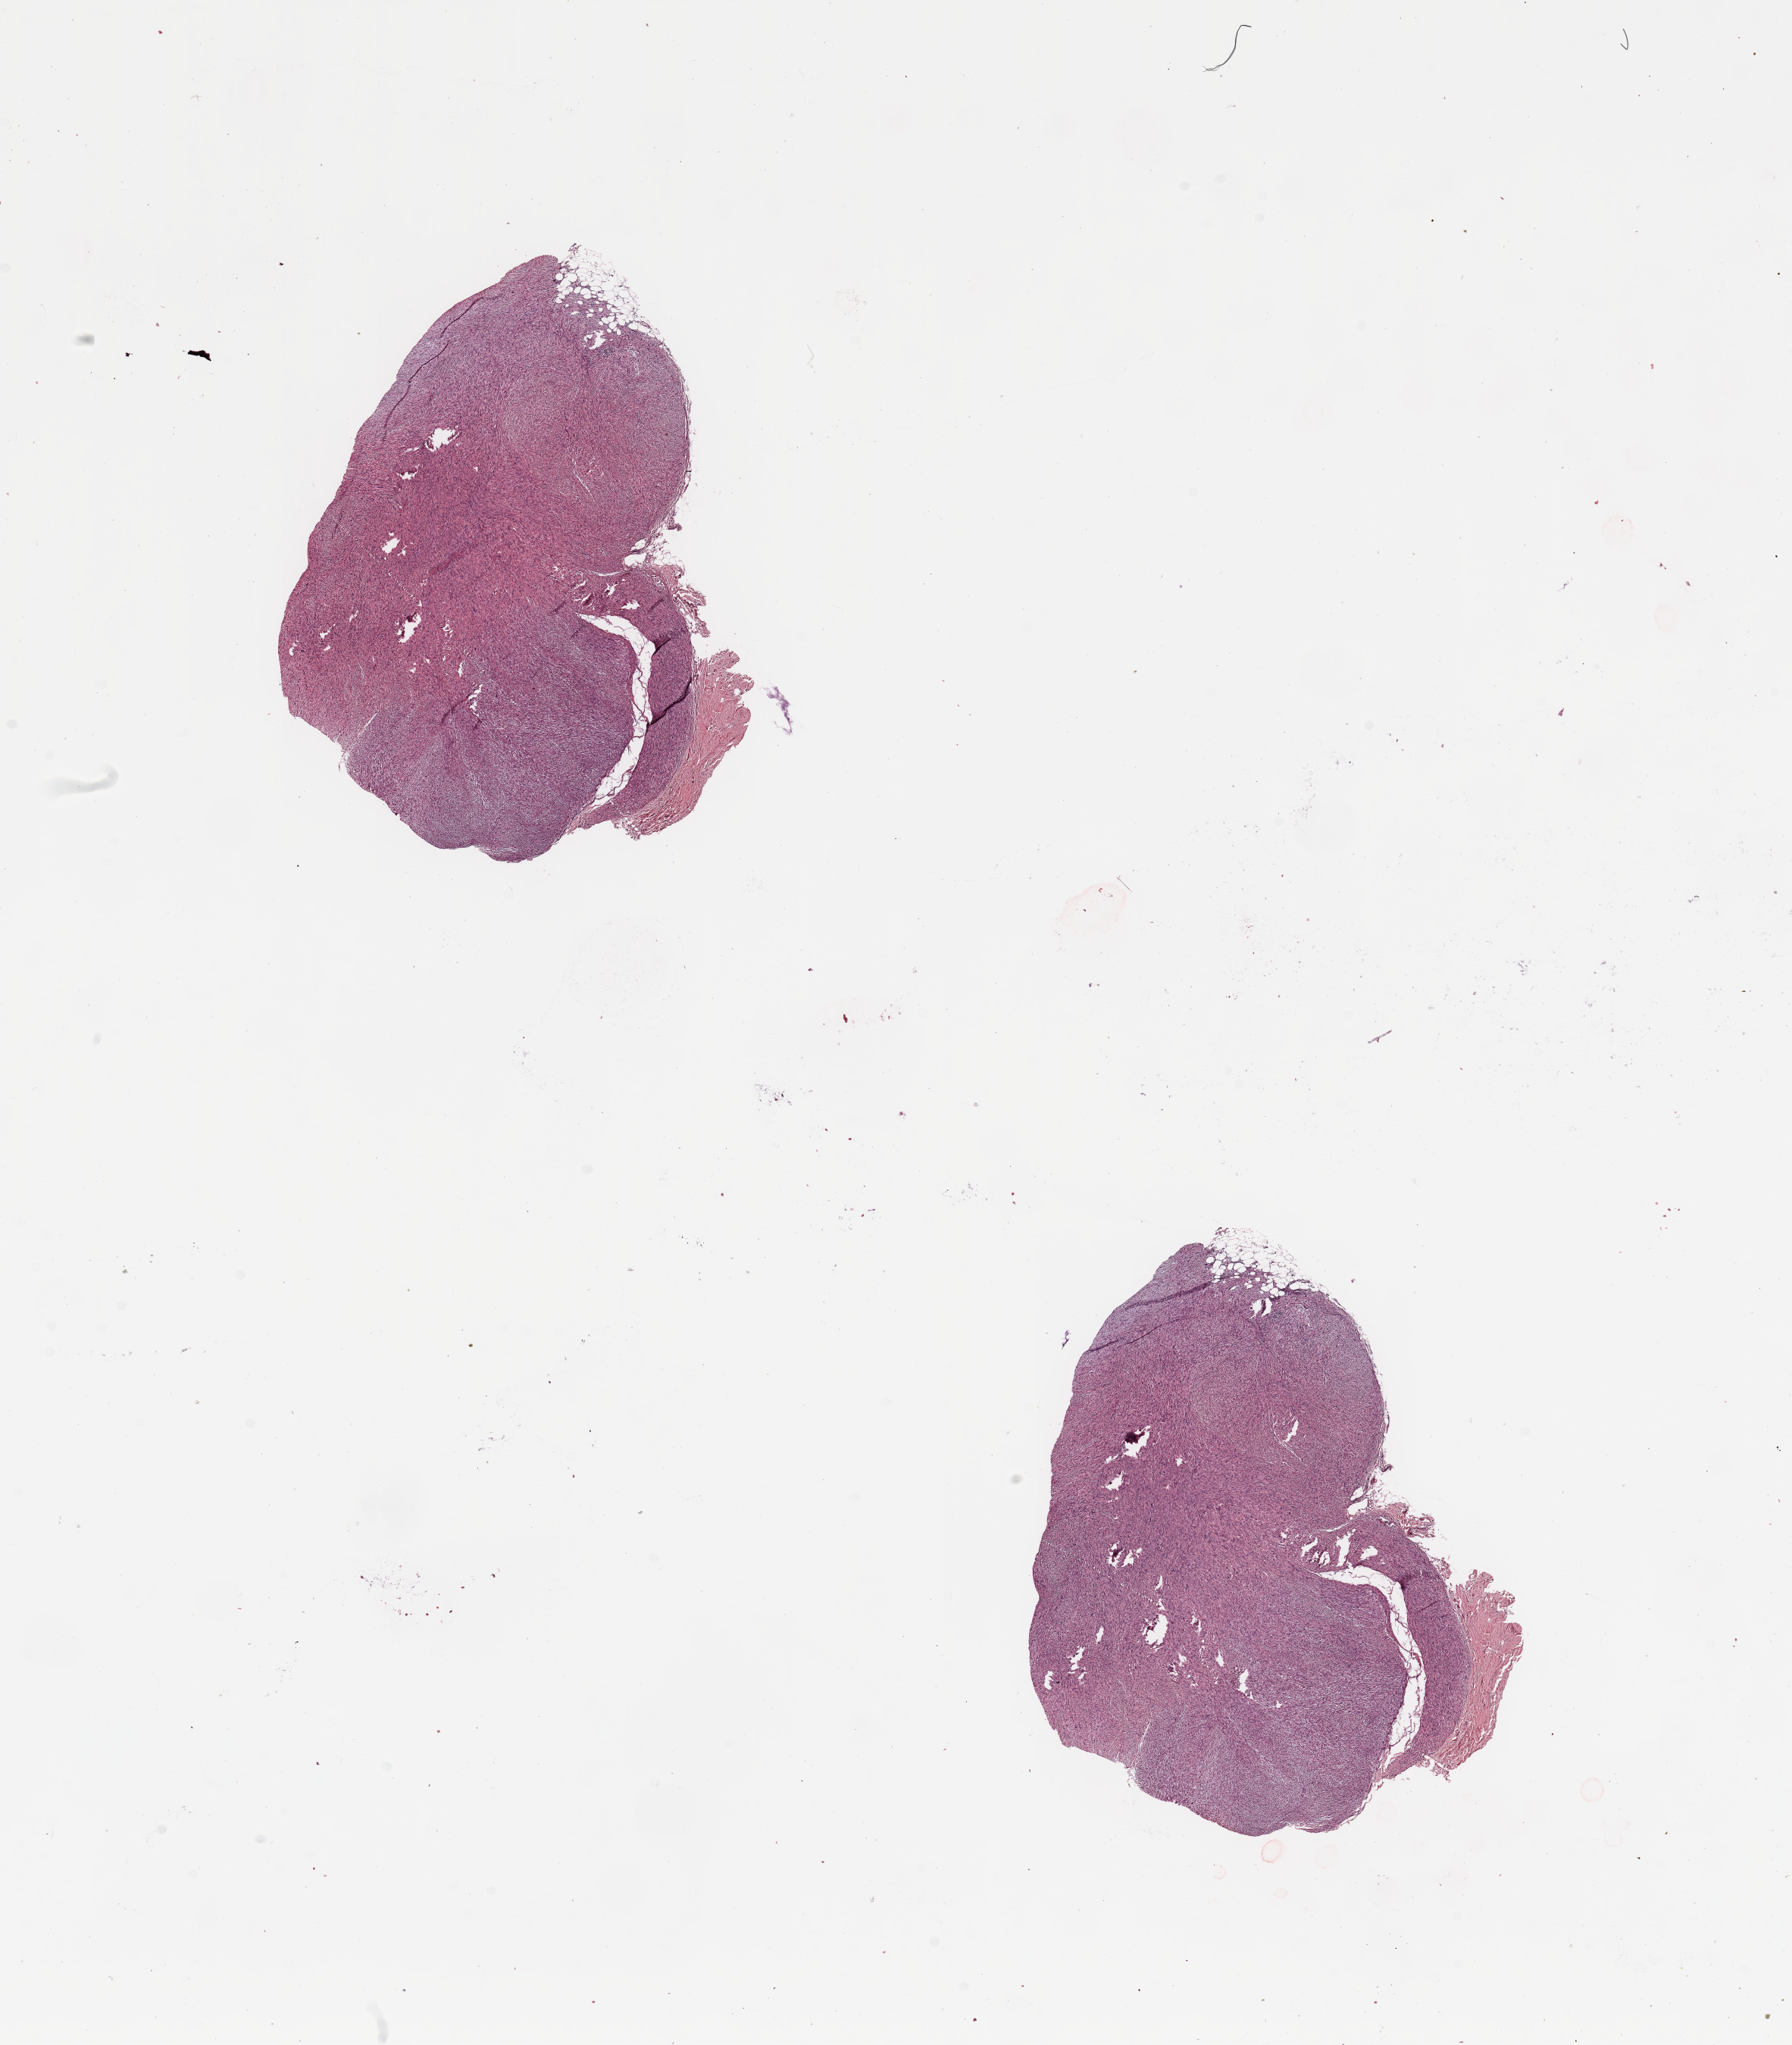
Whole-slide histology image, Hematoxylin and eosin (H&E) stained, a low-resolution overview of the entire scanned area, about 18.7 x 21.3 mm (slide scanned at 20x), tumour tissue sample. 76-year-old female patient.
Patient diagnosis (cohort enrolment): sarcoma (site not recorded at cohort level). Primary tumour site (as recorded): superficial trunk.